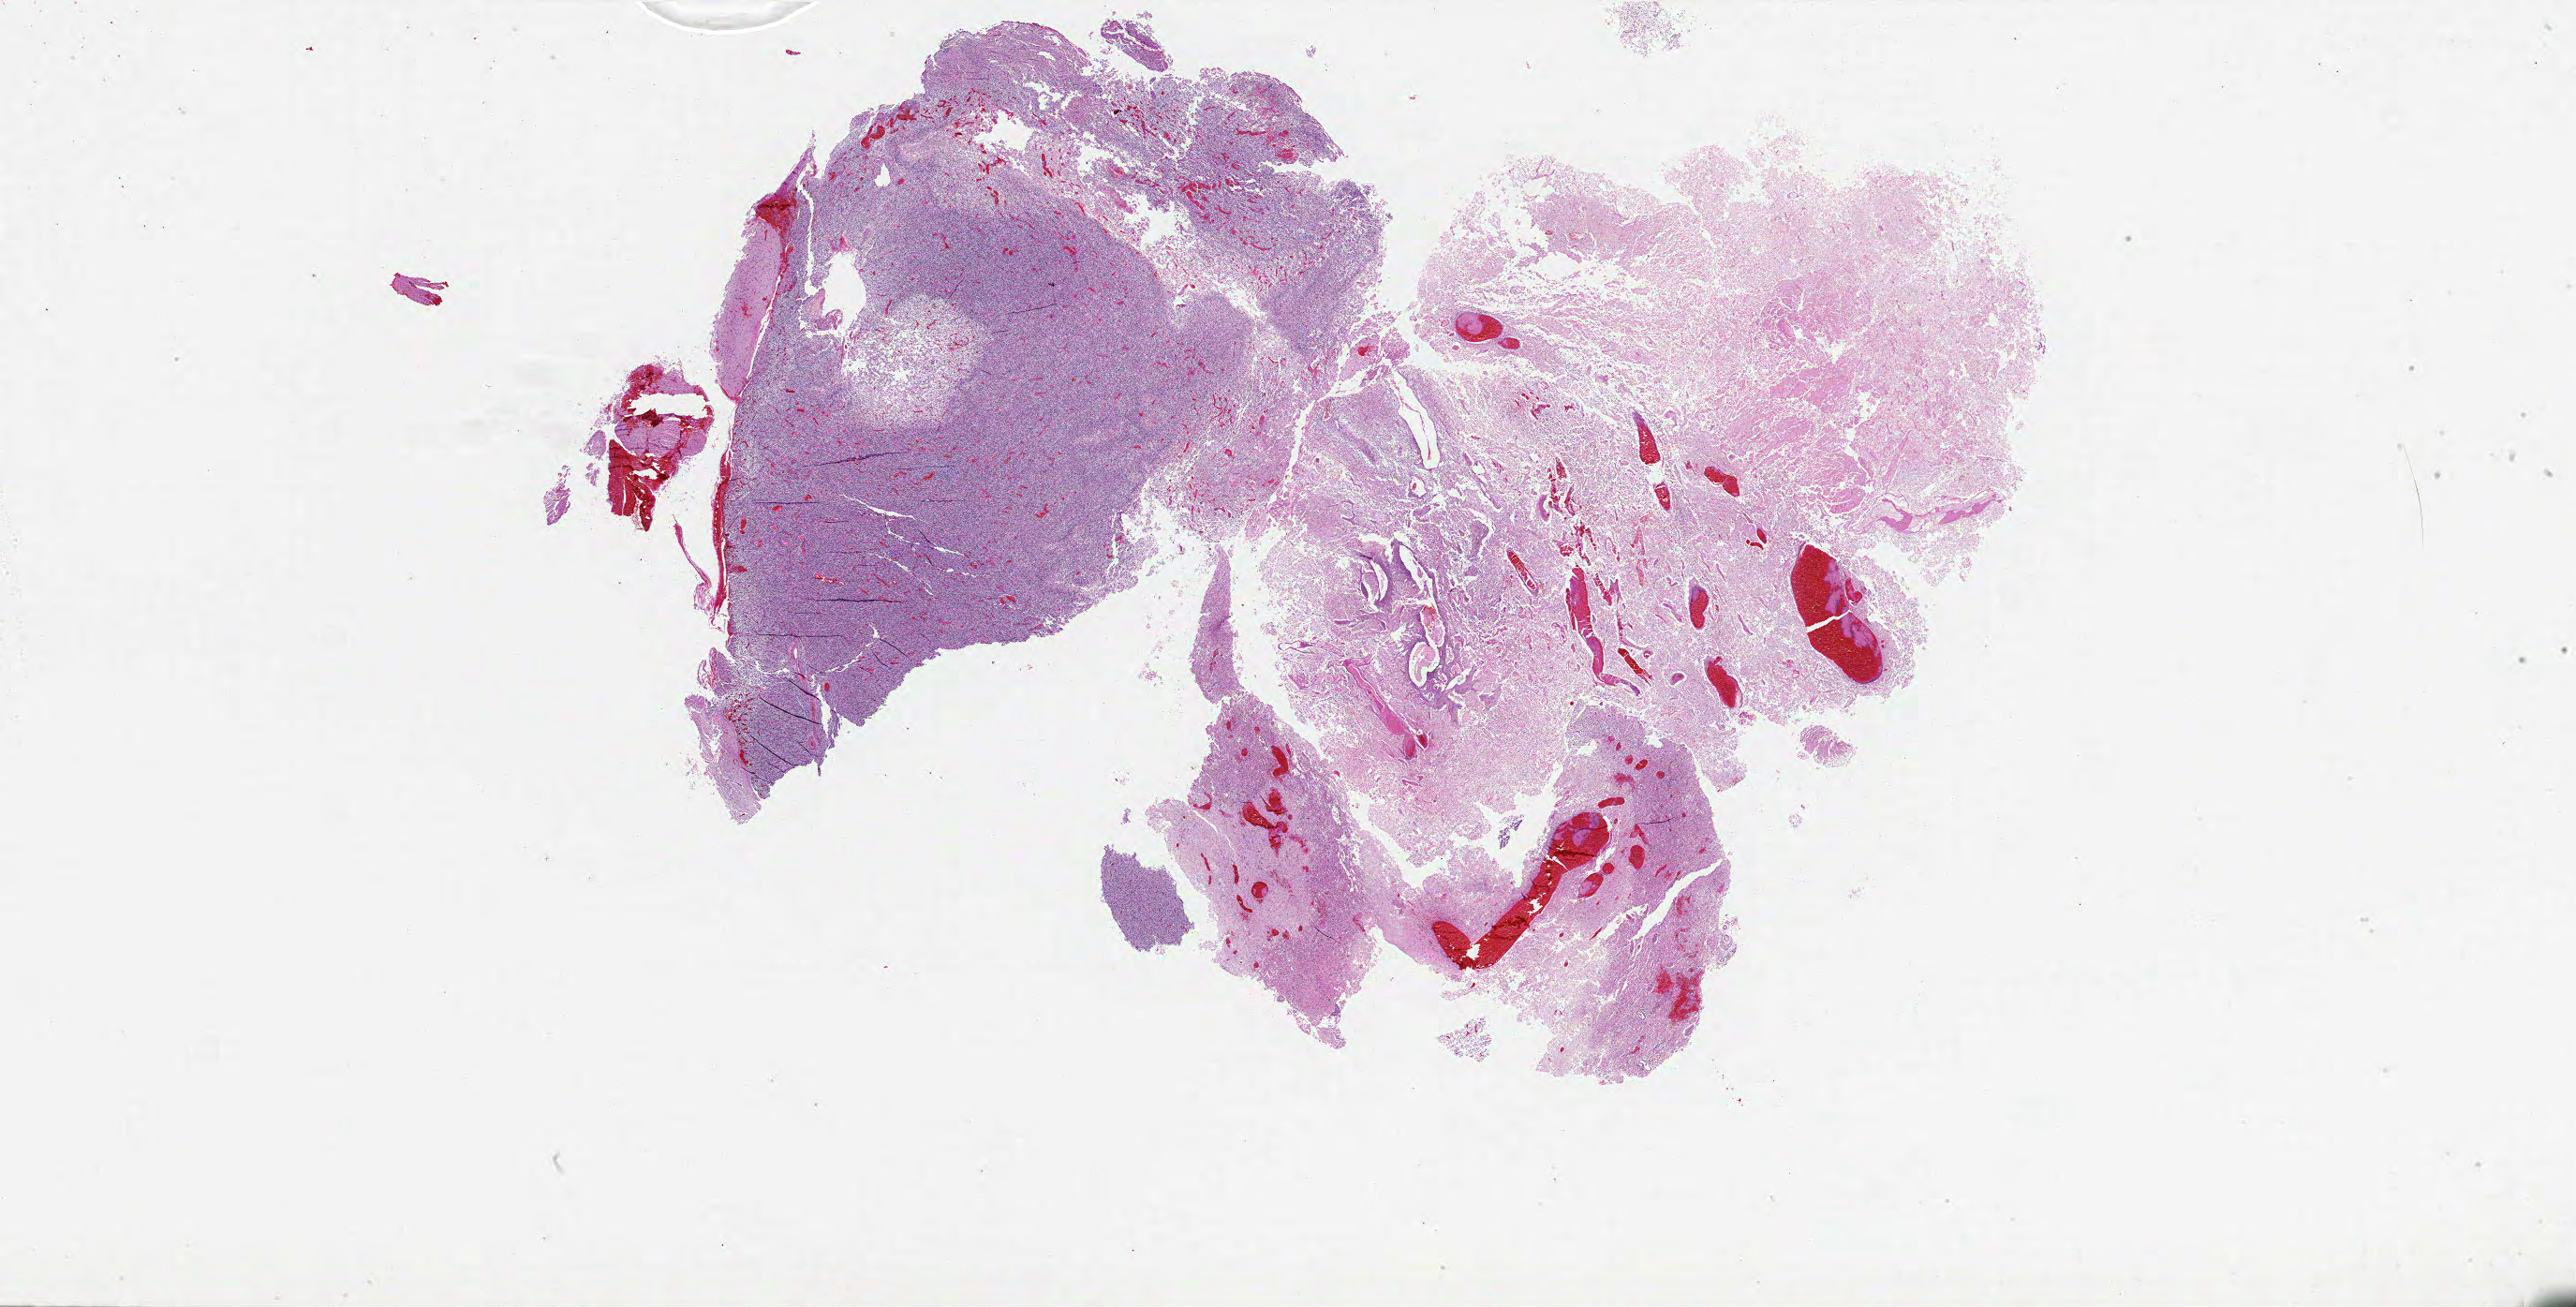
Whole-slide histology image, Hematoxylin and eosin (H&E) stained — whole scanned area (about 44.0 x 22.3 mm) shown as a low-resolution overview; FFPE section; sample: primary tumour, brain. Patient: male, age at initial diagnosis 56 years.
• diagnosis: Glioblastoma